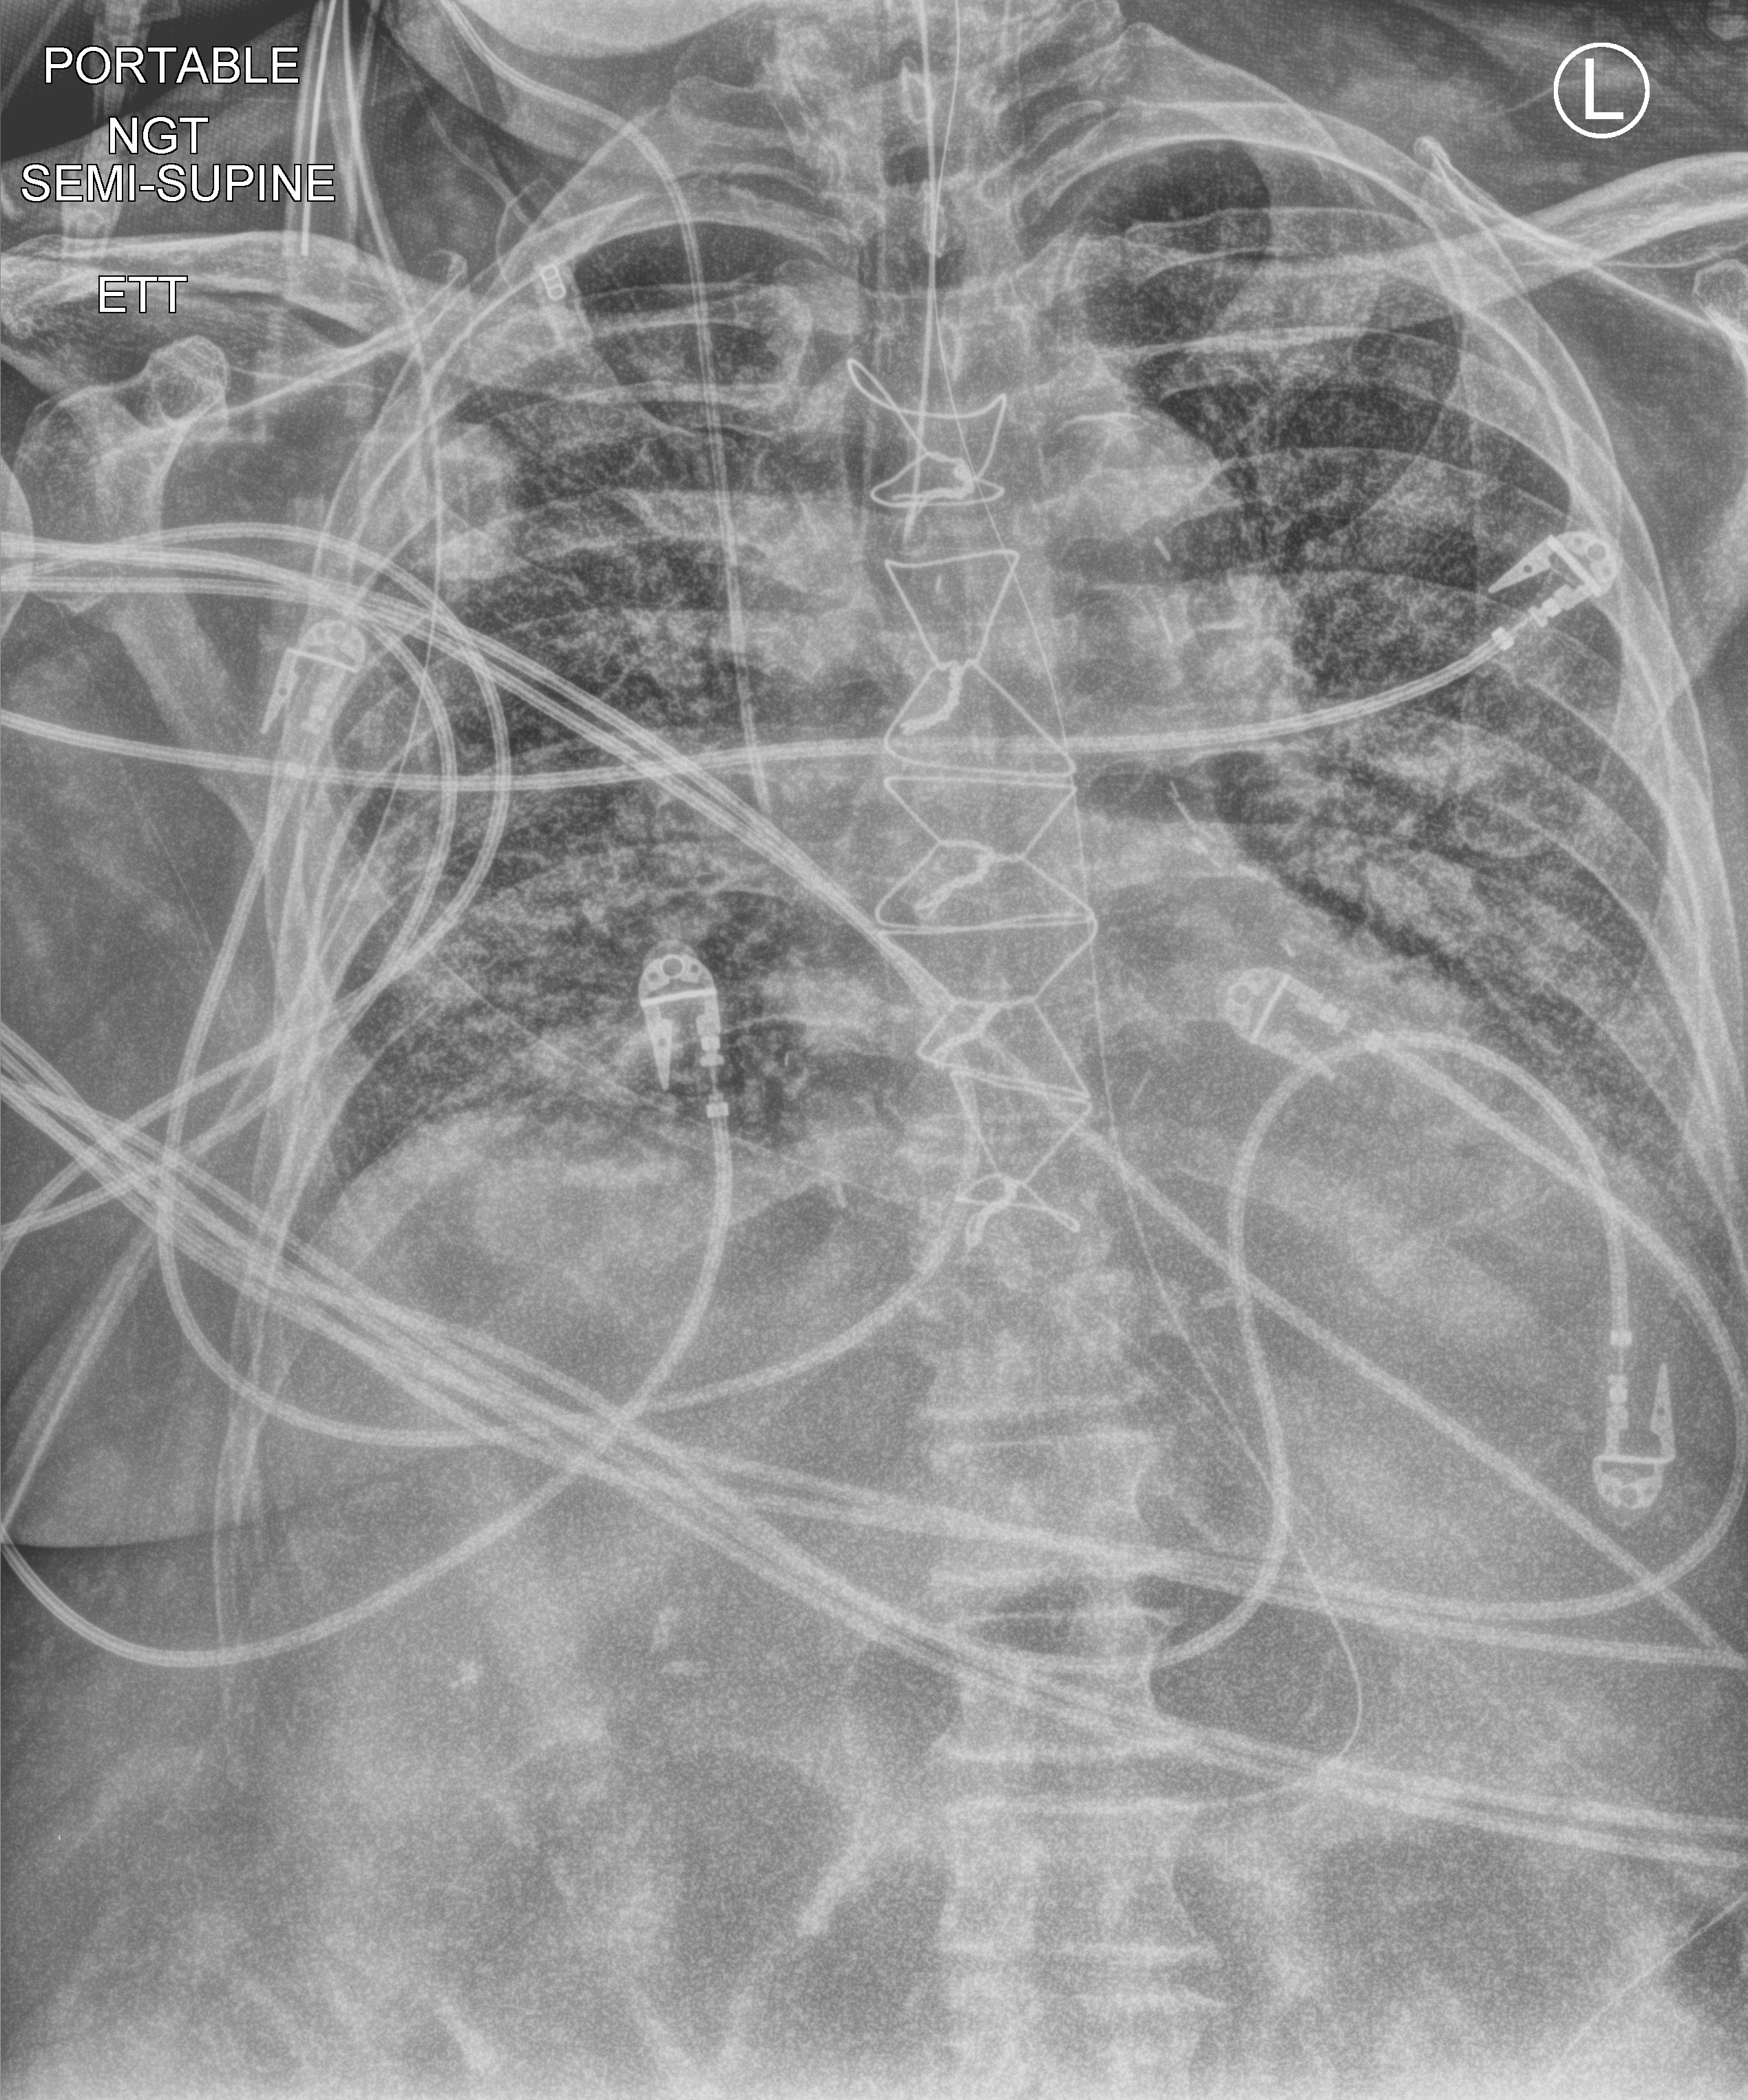
Chest X-ray (portable), anteroposterior (AP) projection. Male patient hospitalised with COVID-19, age 75–90 years.
Admission-level facts for this patient (not findings on this image; timing relative to this image not recorded): length of hospital stay: 28 days; mechanically ventilated during this hospital stay: yes.